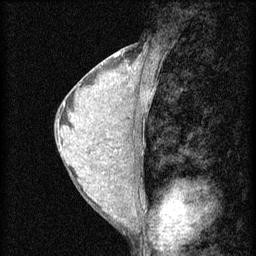
Breast MRI (dynamic contrast-enhanced), one sagittal slice; position 30 of 60 along the scan axis; 3 images stored at this slice position (order not interpretable as contrast timing); 1.5 T; TE 4.2 ms, TR 8.2 ms; 2 mm slice thickness; 256 × 256 image matrix, field of view 180 × 180 mm. Female patient, age 38 years.
Outlined on this slice (semi-automatically segmented with operator editing):
- analysis volume of interest (the breast-tissue region the enhancement analysis was run in; not a lesion): box from (x=115, y=94) to (x=151, y=139) px
- tumour enhancement mask (voxels above the 70 % enhancement threshold inside the analysis volume of interest): (x=144, y=94)–(x=150, y=103)